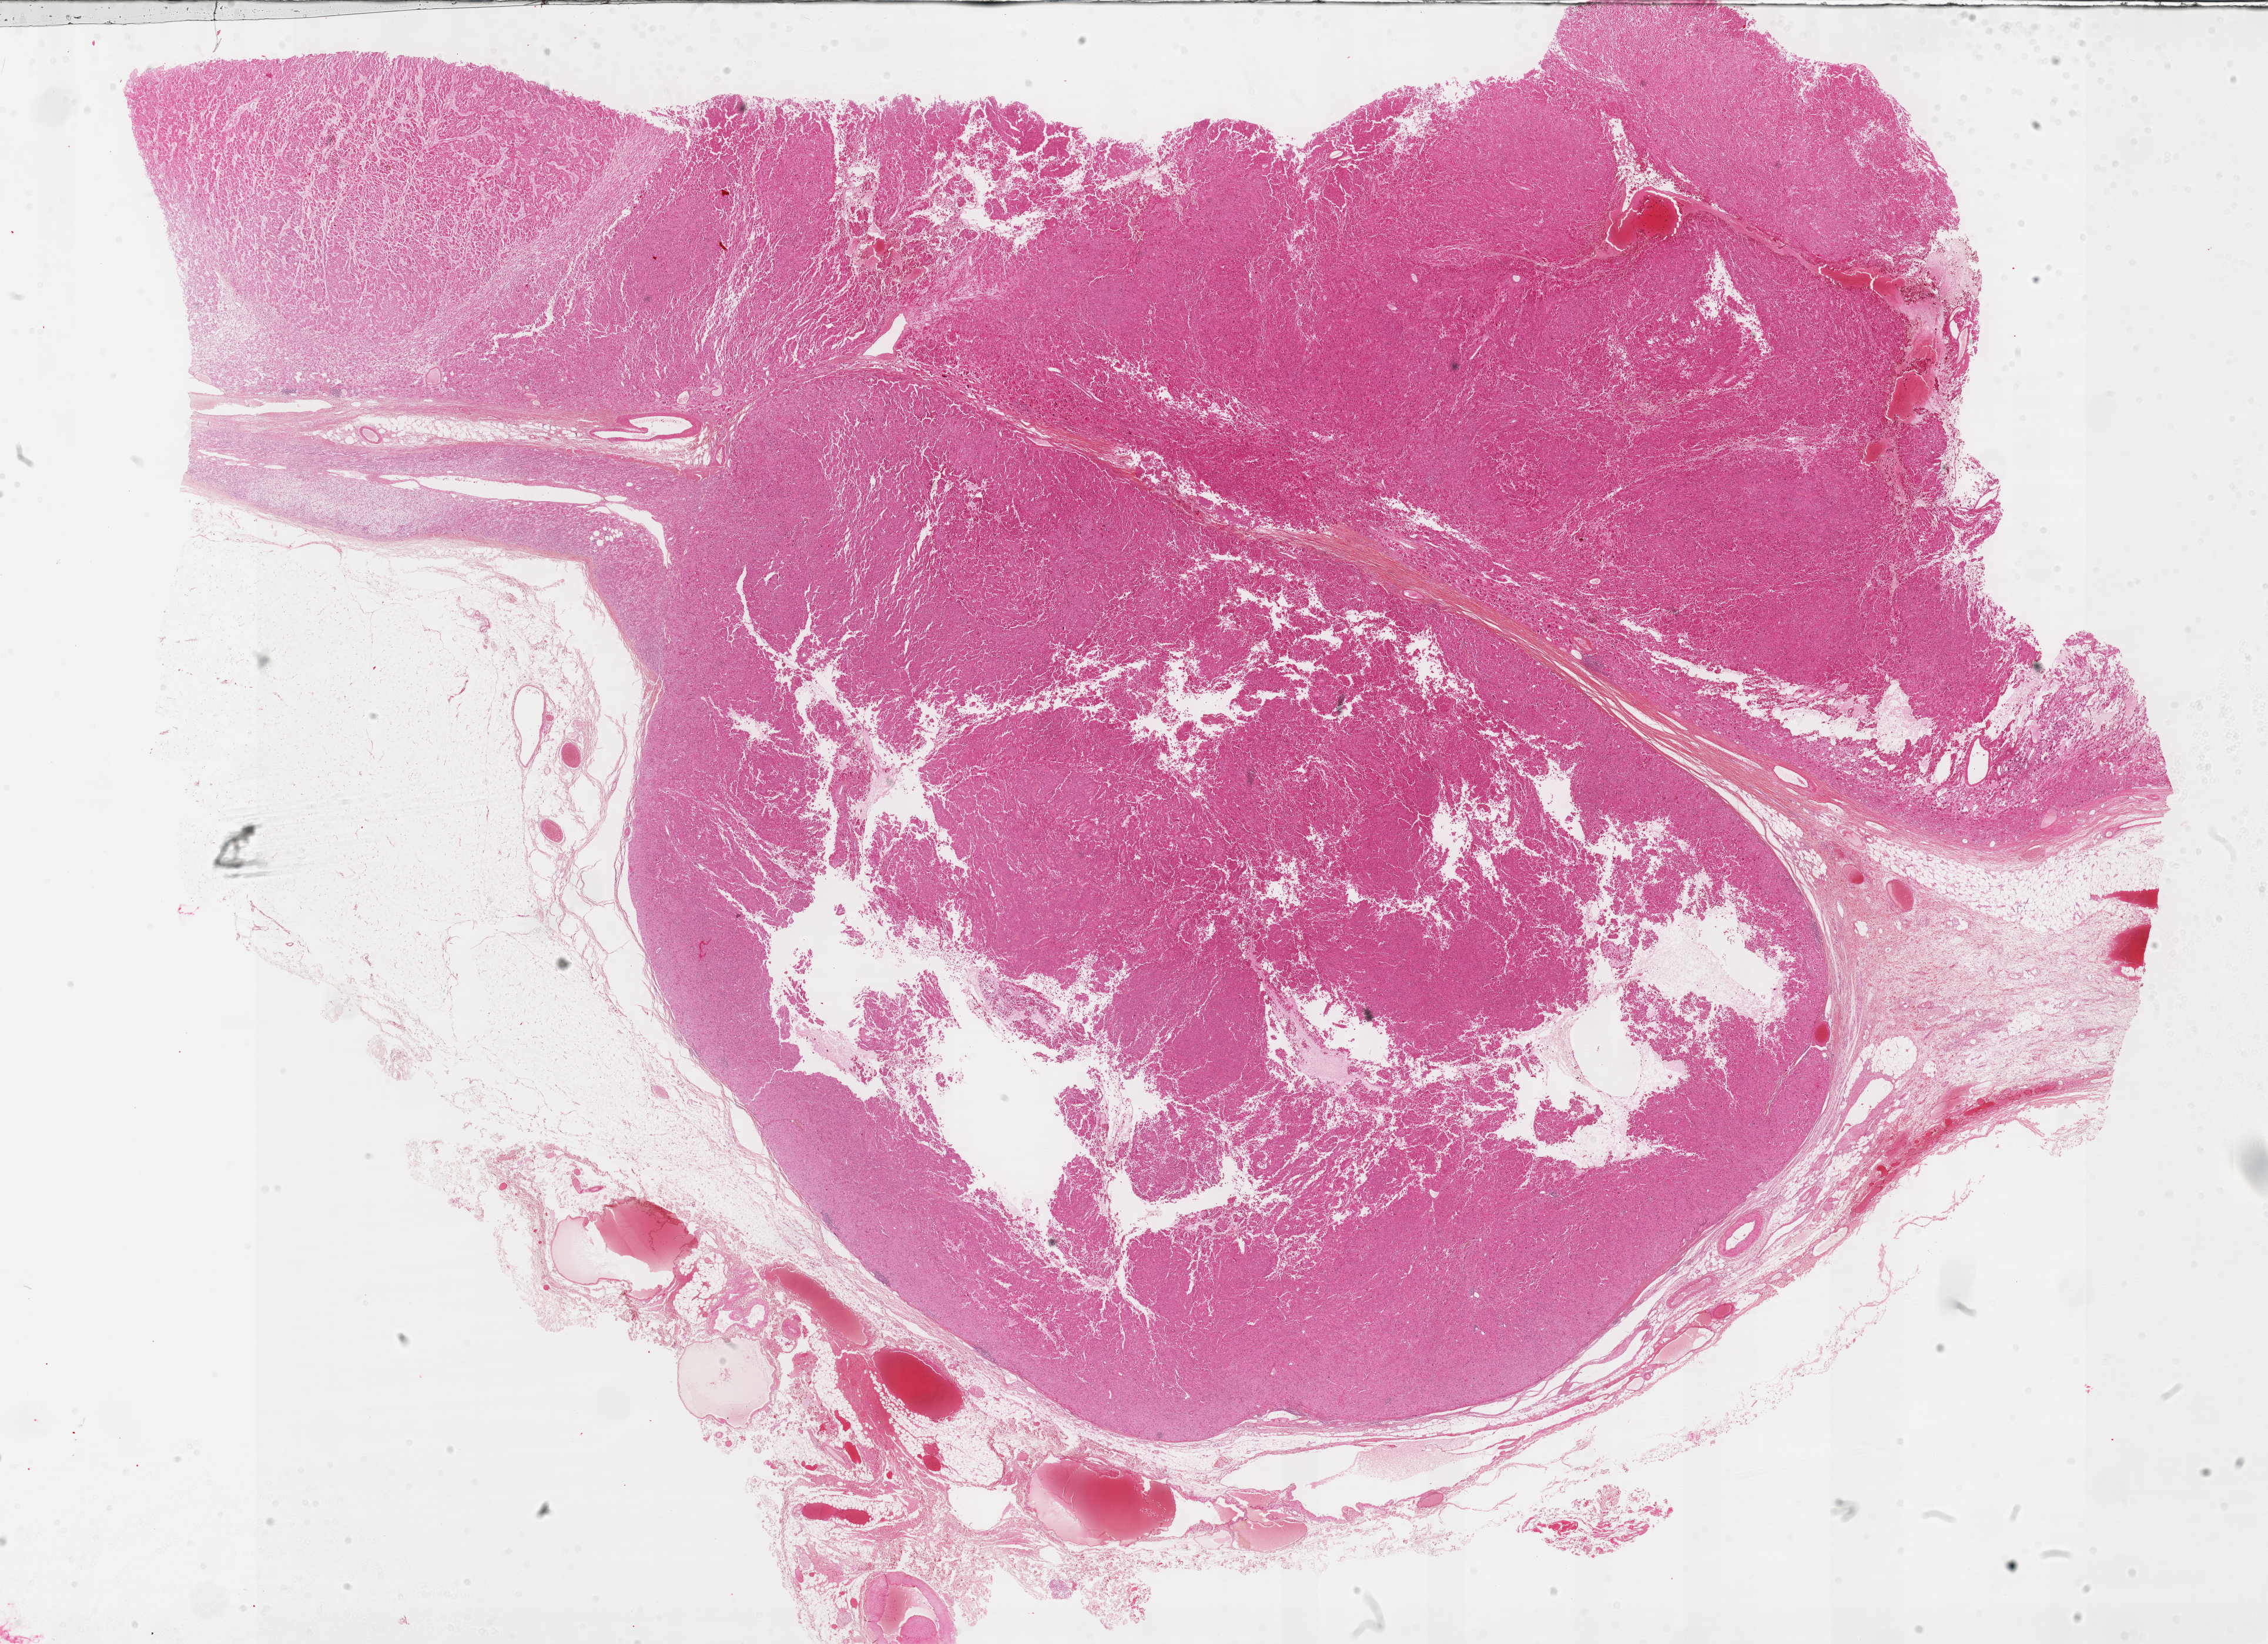
Digitized H&E tissue section (whole slide), whole scanned area (about 31.2 x 22.6 mm, from a 40x scan) shown as a low-resolution overview. Formalin-fixed paraffin-embedded (FFPE) diagnostic section. Sample: primary tumour, adrenal cortex. Male patient; age at initial diagnosis 57 years.
Pathologic diagnosis: Adrenal cortical carcinoma (cortex of adrenal gland).